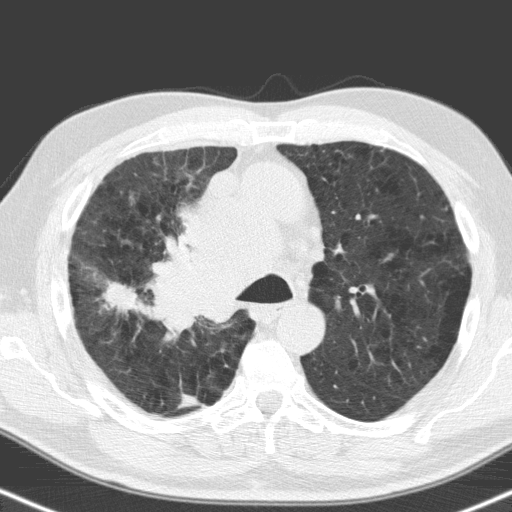
Axial slice from a low-dose chest CT screening exam; baseline screening round; lung window (W 1500 / L -600 HU); 3.2 mm slice thickness. Male, age 71 years at enrolment. Former smoker at enrolment.
Expert-annotated lung lesion, bounding box (x1, y1, x2, y2) in pixels: (89, 271, 164, 338). The screening reader recorded 2 non-calcified nodules or masses ≥4 mm on this exam; which of them this box marks is not recorded. Participant outcome: lung cancer diagnosed 31 days after this screen — small cell carcinoma, NOS, right upper lobe, stage IV (AJCC 6th edition), 40 mm at pathology.